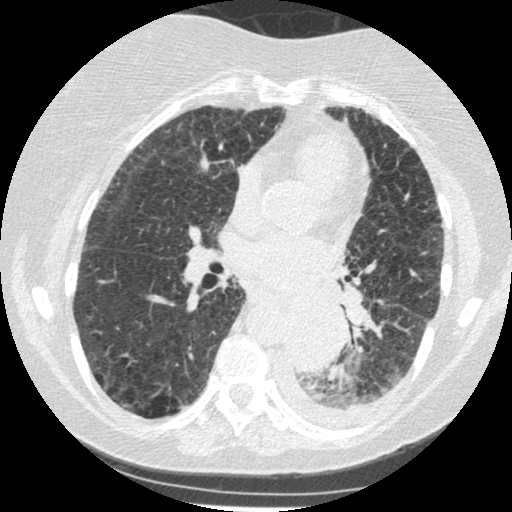
Chest CT (low-dose screening protocol), one axial image; third screening round (two years after baseline); lung window (W 1500 / L -600 HU); 1.25 mm slice thickness; standard (soft-tissue) reconstruction kernel (STANDARD); 512 × 512 image matrix, field of view 310 × 310 mm. Female participant, aged 60 years at enrolment.
Lesion marked by an expert reader, box from (x=274, y=305) to (x=343, y=375) px. Reader record for this screening exam (exam-level; its link to the box is not recorded): non-calcified nodule or mass ≥4 mm, left lower lobe, 54 × 38 mm, smooth margins, soft tissue attenuation, pre-existing on the prior screen: yes; interval growth: yes. Participant outcome: lung cancer diagnosed 15 days after this screen — small cell carcinoma, NOS, left lower lobe, undifferentiated (G4), stage IV (AJCC 6th edition), 69 mm at pathology.